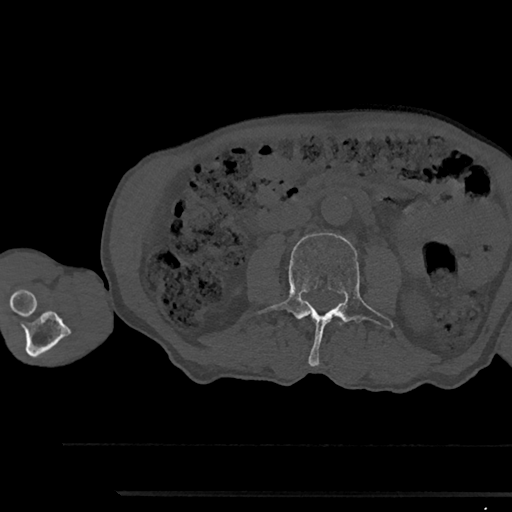
CT including the spine, one axial slice; slice 495 of 797 in the series (ordered by position); reconstruction kernel Br40s/3; bone window (W 1800 / L 400 HU); 0.5 mm slice thickness; 512 × 512 image matrix, field of view 367 × 367 mm. Male patient, age 79 years. From the clinical record (not read from this slice): primary cancer: prostate.
Annotated regions visible in this slice (semi-automatically segmented with operator editing):
- L3 vertebra: box from (x=254, y=233) to (x=393, y=366) px